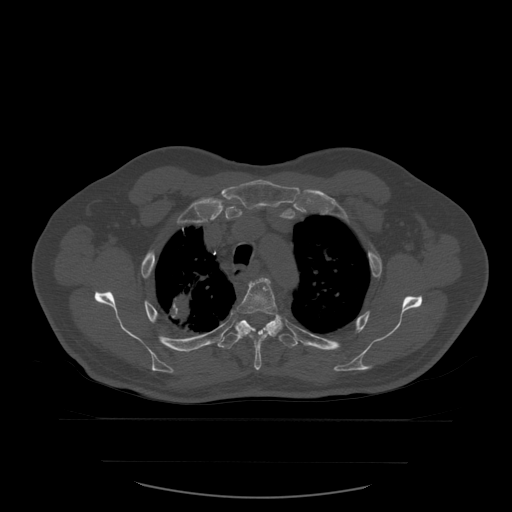
CT including the spine, one axial slice; position 437 of 590 along the scan axis; bone window (W 1800 / L 400 HU); 512 × 512 image matrix. Patient age 71 years. From the clinical record (not read from this slice): primary cancer: lung; vertebrae with lytic lesions (as recorded): T1, T2, L5, S1.
Outlined on this slice (semi-automatically segmented with operator editing):
- T4 vertebra: box from (x=237, y=278) to (x=283, y=371) px
- T5 vertebra: (x=218, y=320)–(x=299, y=350)